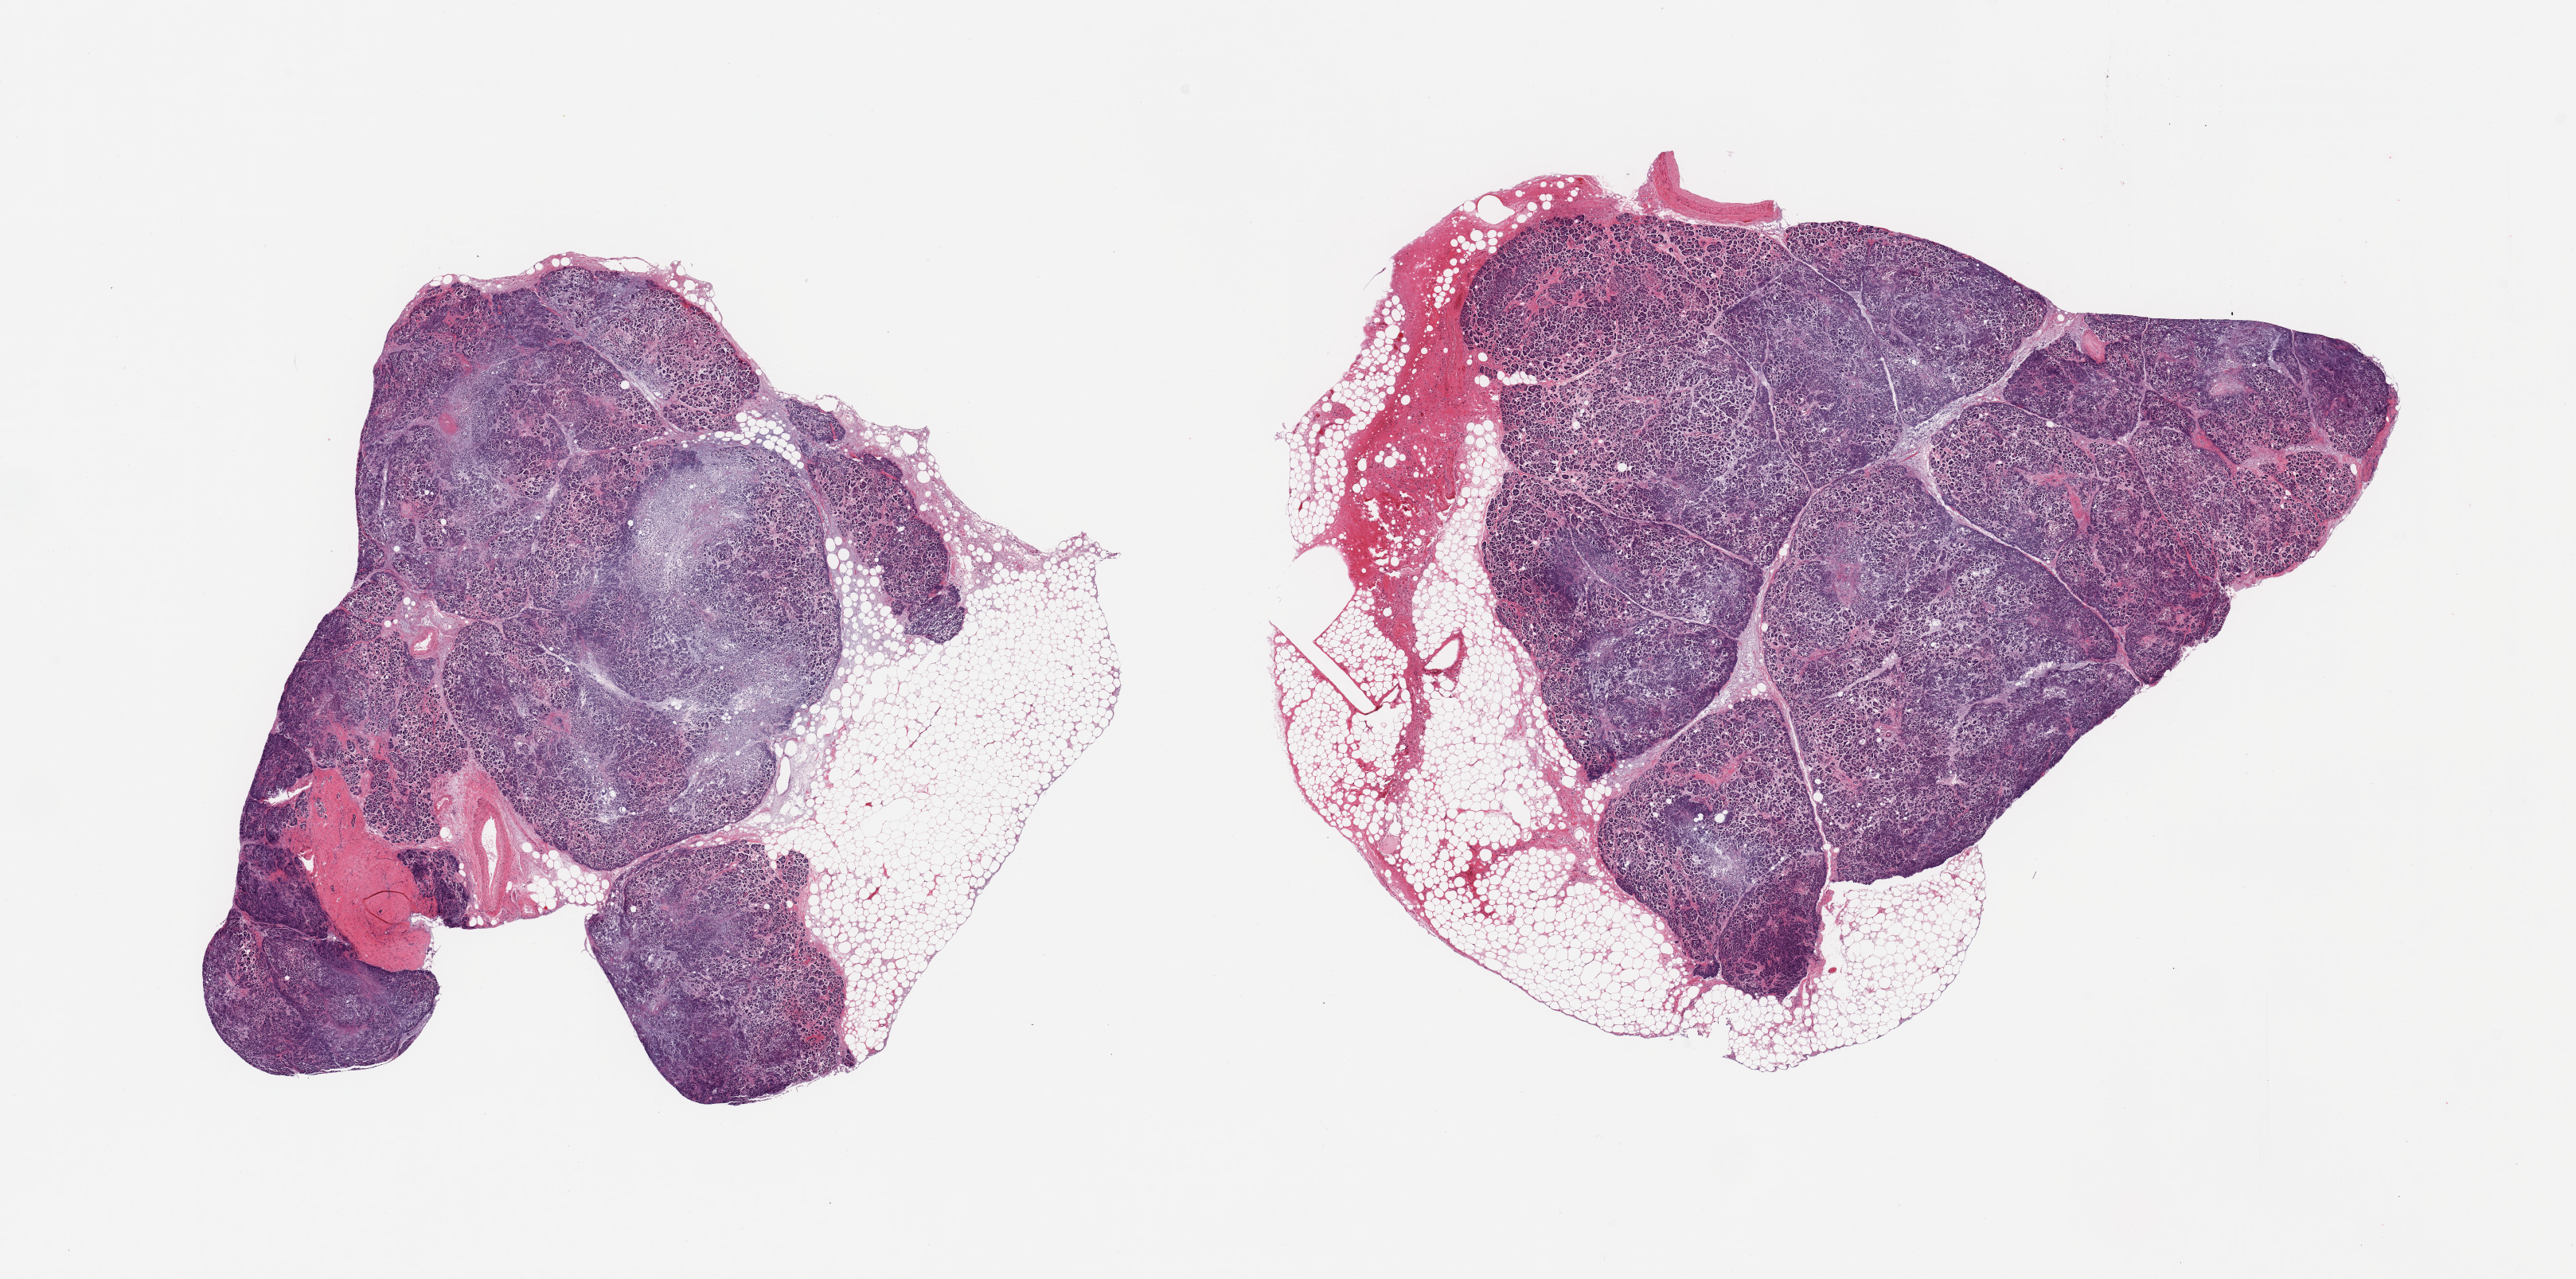
Whole-slide image, H&E stain — low-resolution overview of the scanned area, about 25.6 x 12.7 mm (slide scanned at 20x). PAXgene-fixed, paraffin-embedded tissue. Target tissue: pancreas. Donor tissue sample.
Review note (as recorded): 2 pieces; parenchyma autolyzed; 30% extraneous fat.